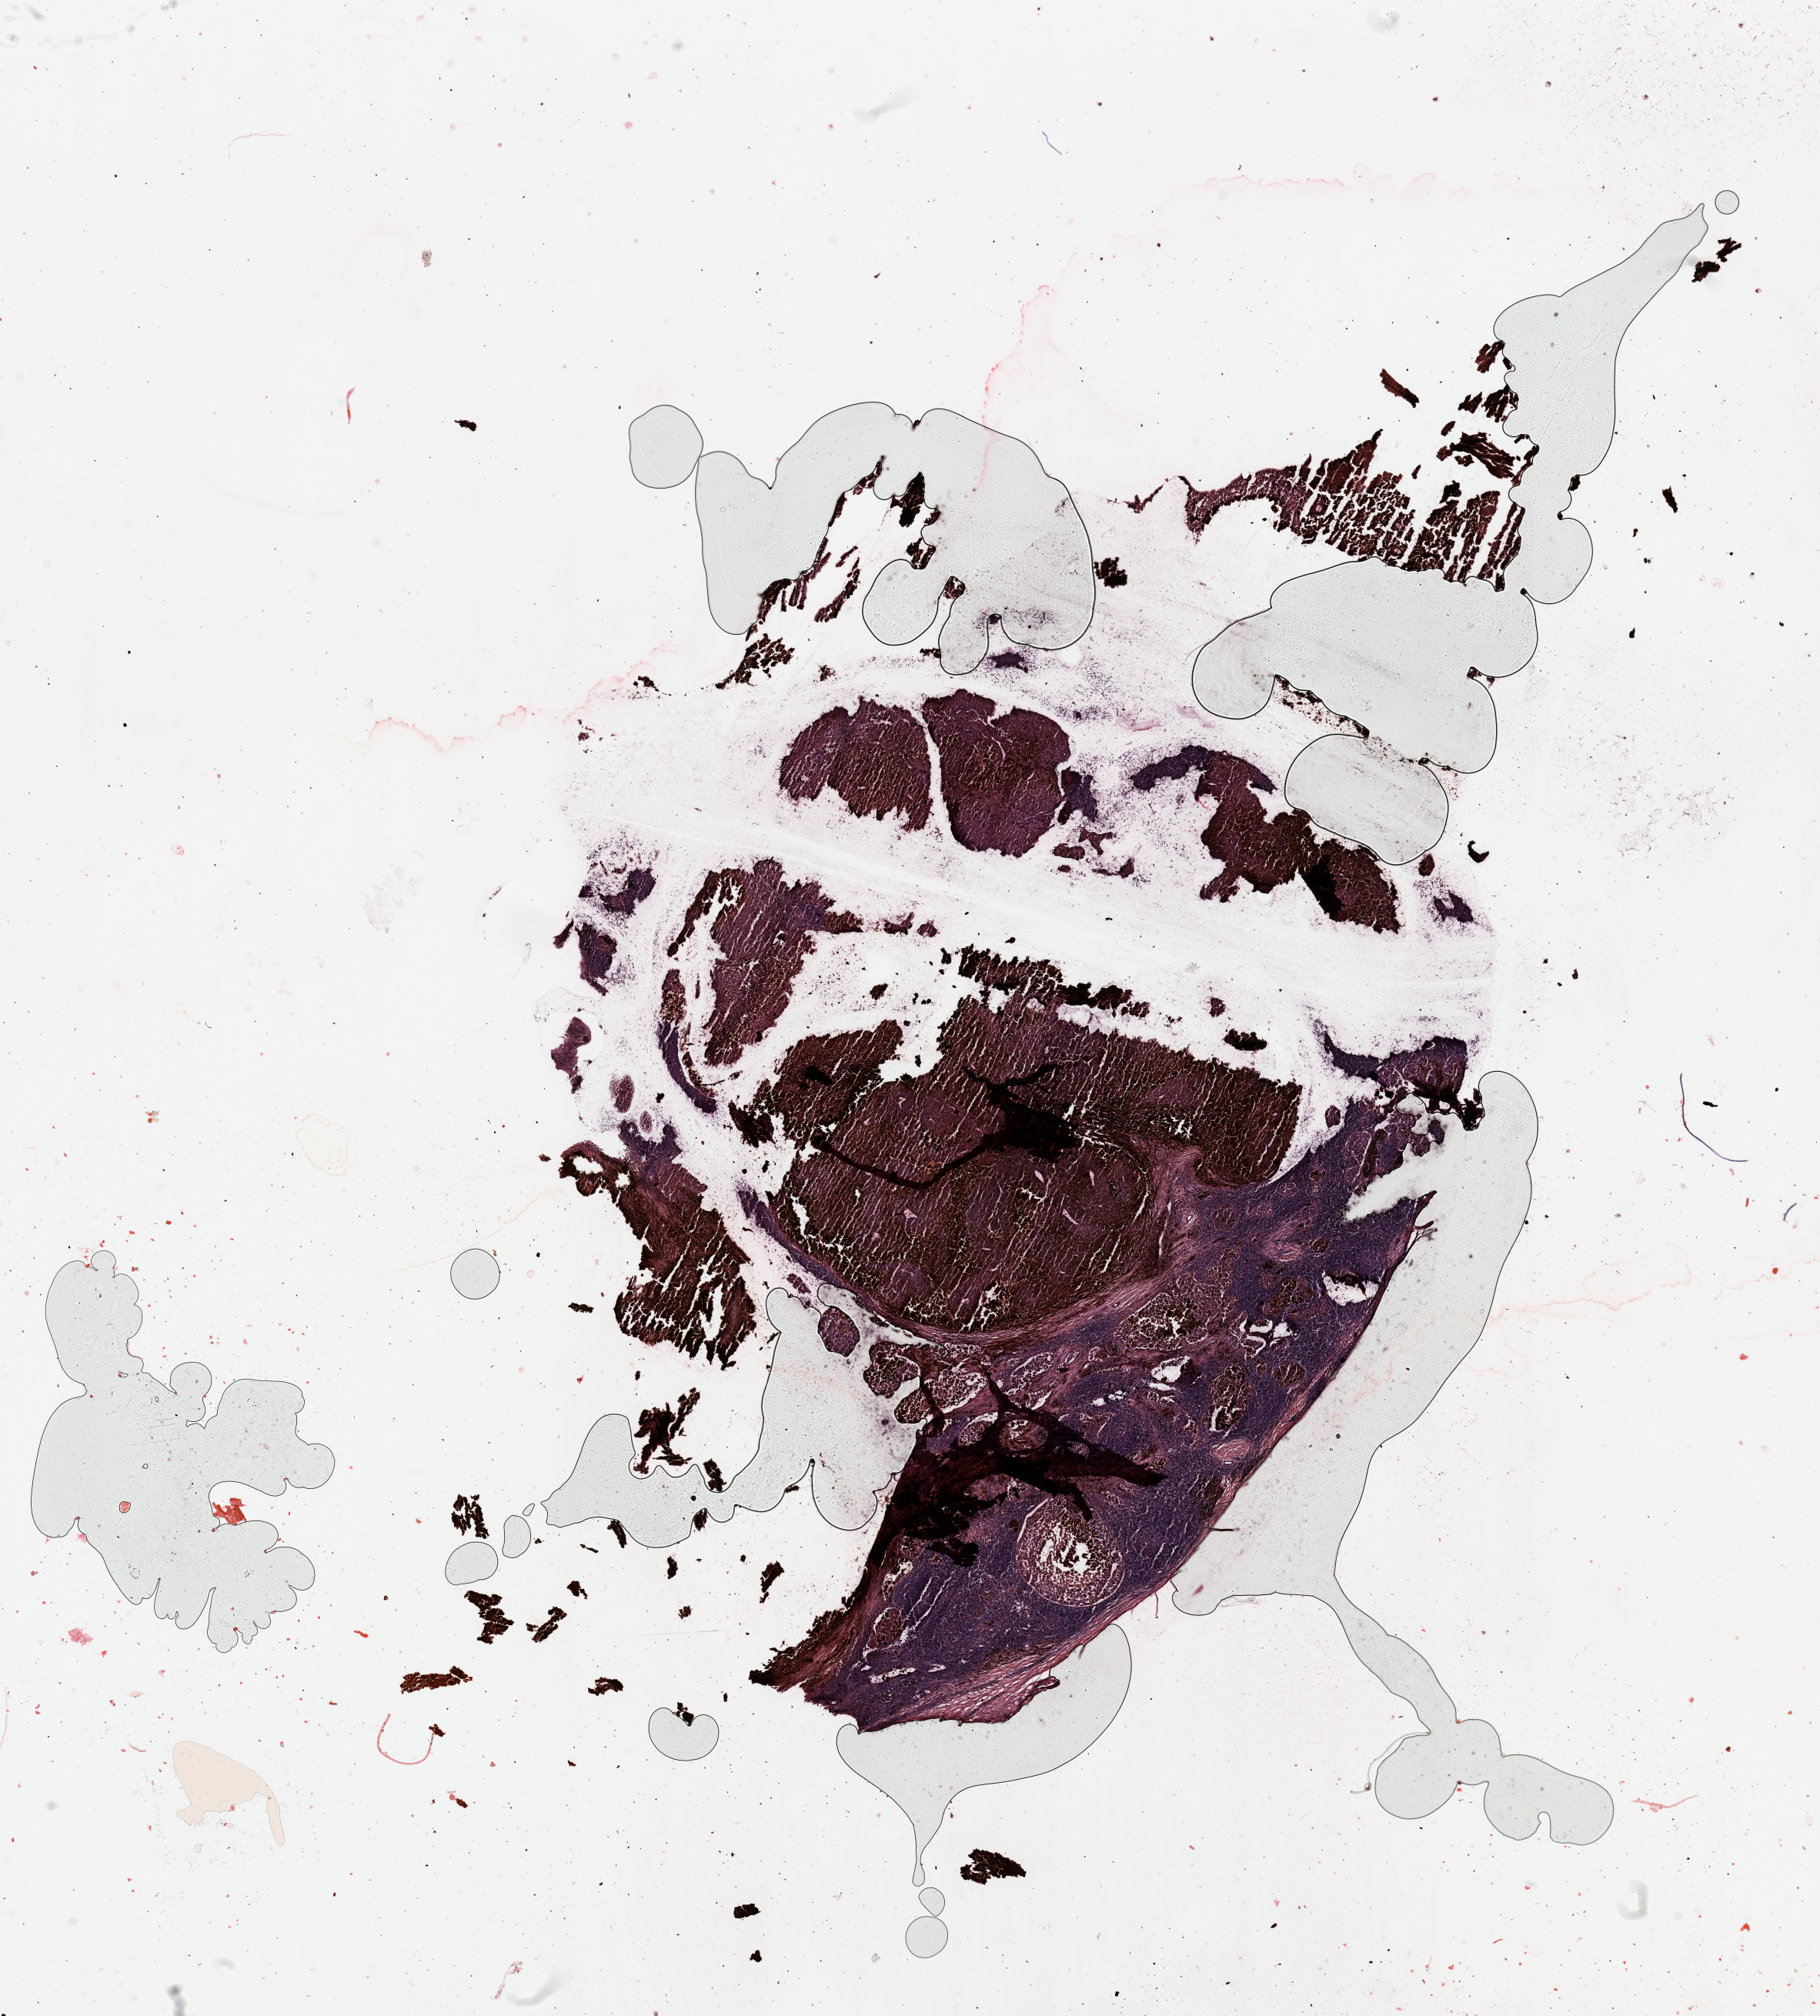
Hematoxylin and eosin (H&E) stained whole-slide image, whole scanned area (about 18.7 x 20.7 mm, from a 20x scan) shown as a low-resolution overview, melanoma tumour tissue; sampled site not recorded. Patient: female, age 23 years.
Patient diagnosis (cohort enrolment): cutaneous melanoma (skin).